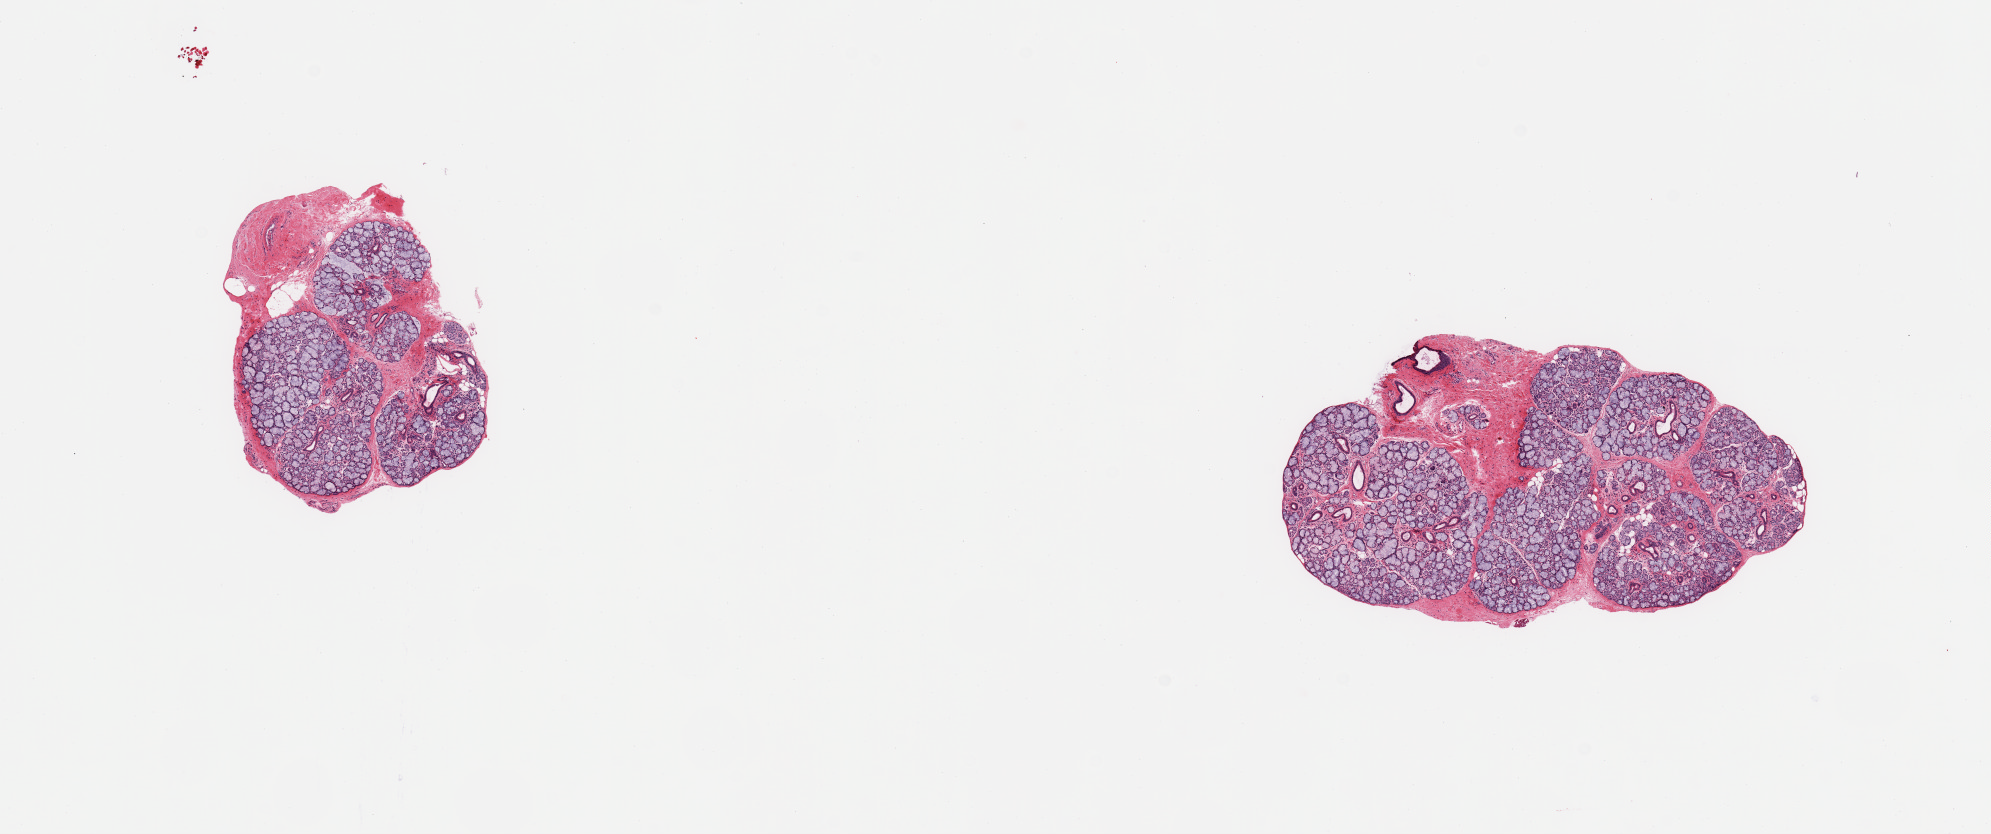
Digitized H&E-stained section — low-resolution overview of the scanned area, about 15.8 x 6.6 mm, PAXgene-fixed, paraffin-embedded tissue, target tissue: minor salivary gland, donor tissue sample. Male donor.
Reviewer comment on this tissue sample: 2 pieces; salivary gland elements with minimal attached stroma.